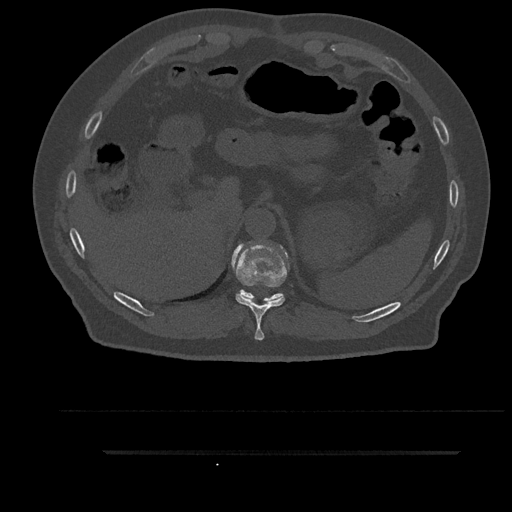
CT including the spine, one axial slice; slice 343 of 797 in the series (ordered by position); 120 kVp; bone window (W 1800 / L 400 HU); 0.5 mm slice thickness; 512 × 512 image matrix. Patient: male, 63 years. From the clinical record (not read from this slice): primary cancer: renal.
Outlined on this slice (semi-automatic segmentation, software-assisted and operator-edited):
- T10 vertebra: bounding box (x1, y1, x2, y2) in pixels: (231, 243, 289, 340)
- T11 vertebra: (237, 290, 283, 302)